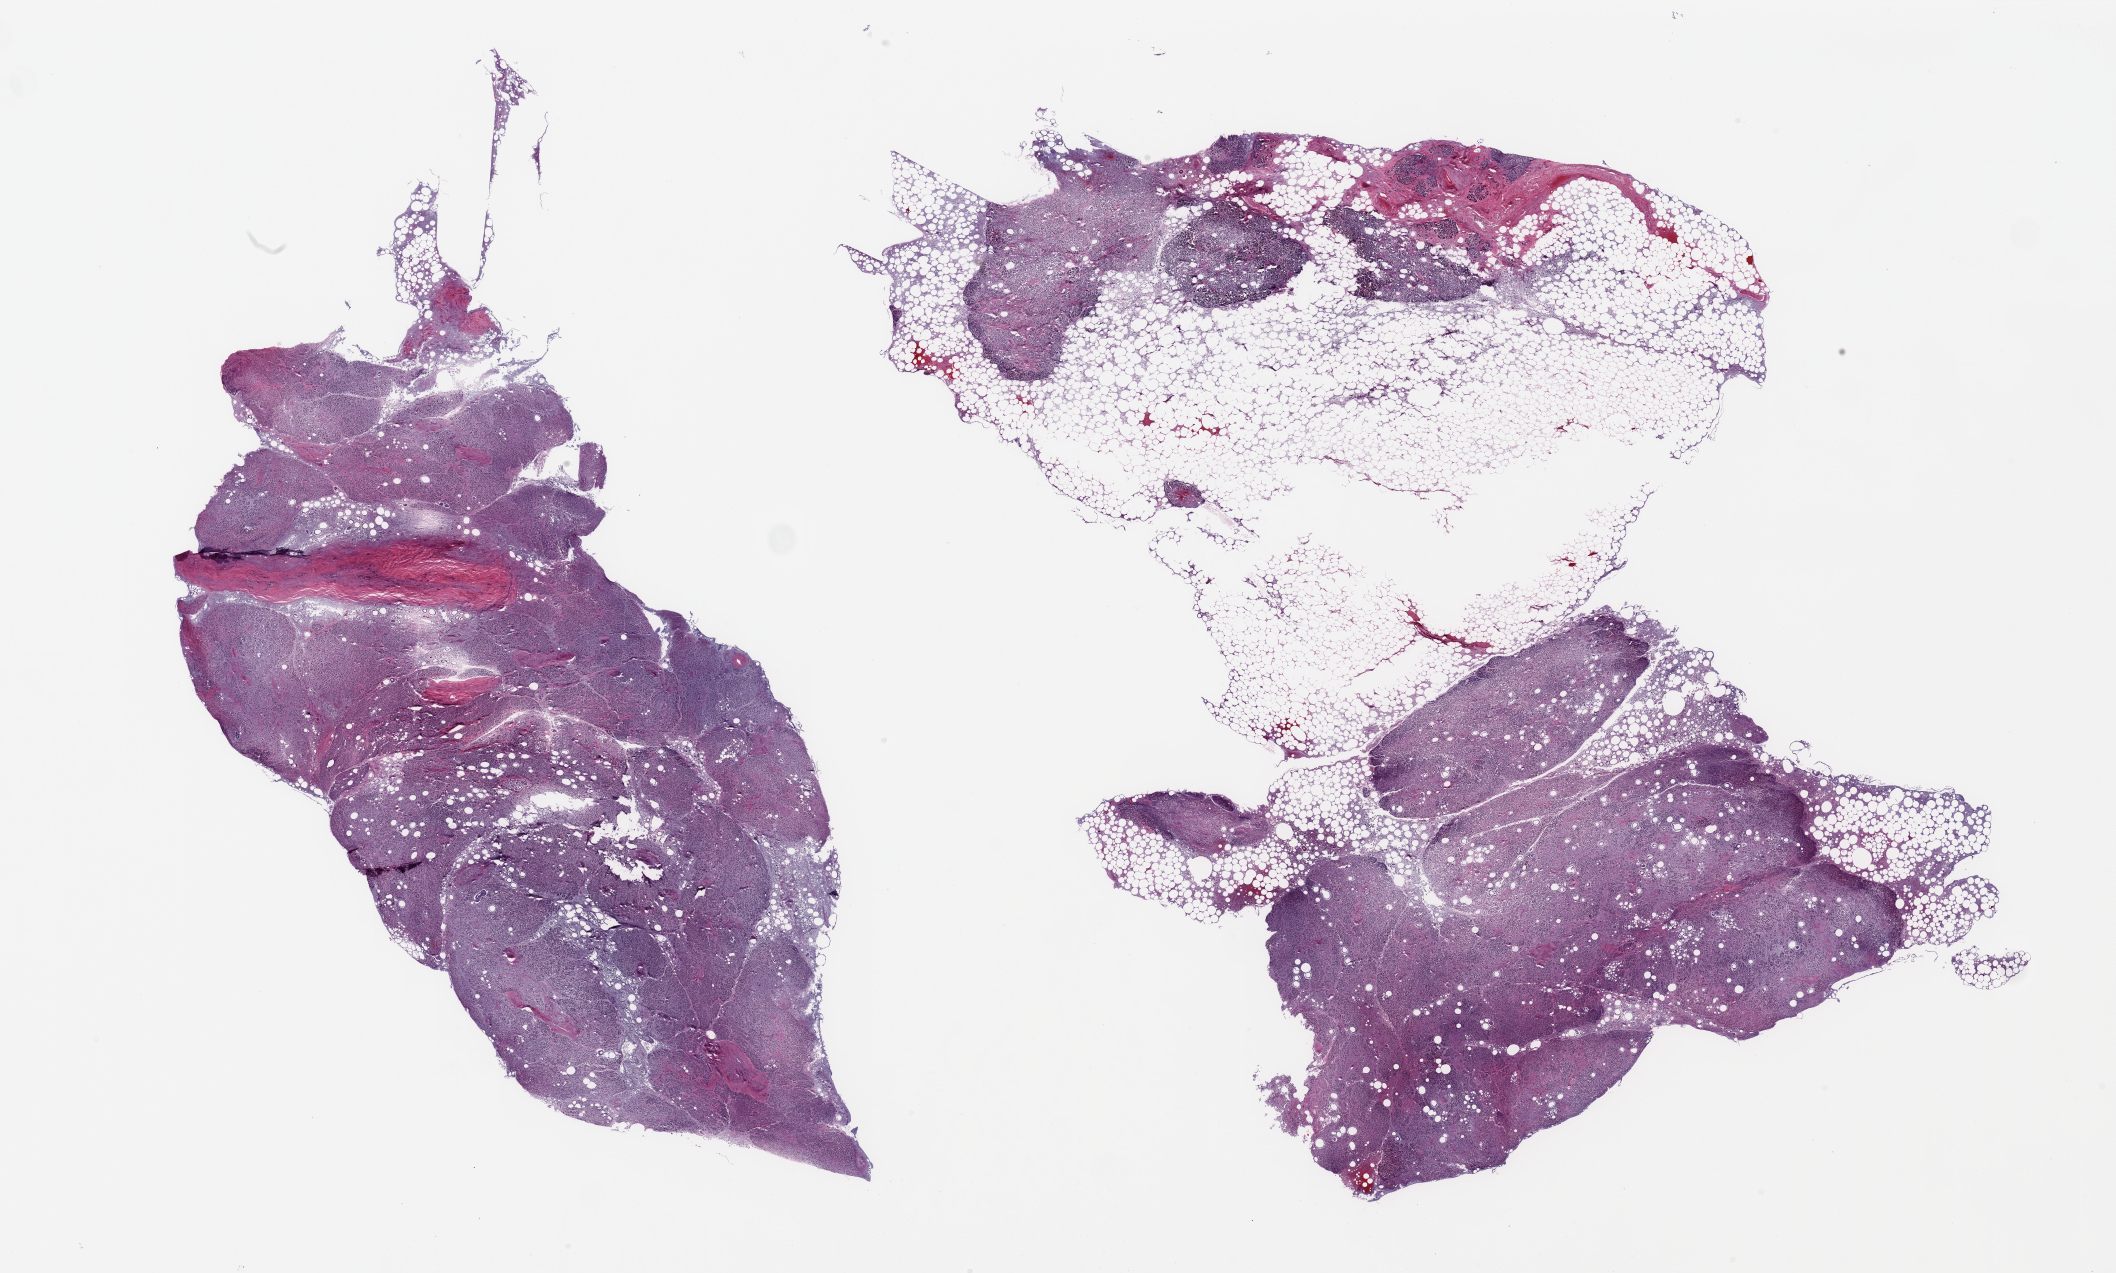
H&E whole-slide image, low-resolution overview of the scanned area, about 33.5 x 20.1 mm, PAXgene-fixed paraffin-embedded (PFPE) section, target tissue: pancreas, tissue donor sample. Donor sex: male.
Pathologist's review note for this sample: 3 pieces, advanced saponifcation, ~40% fat, islets not visible.